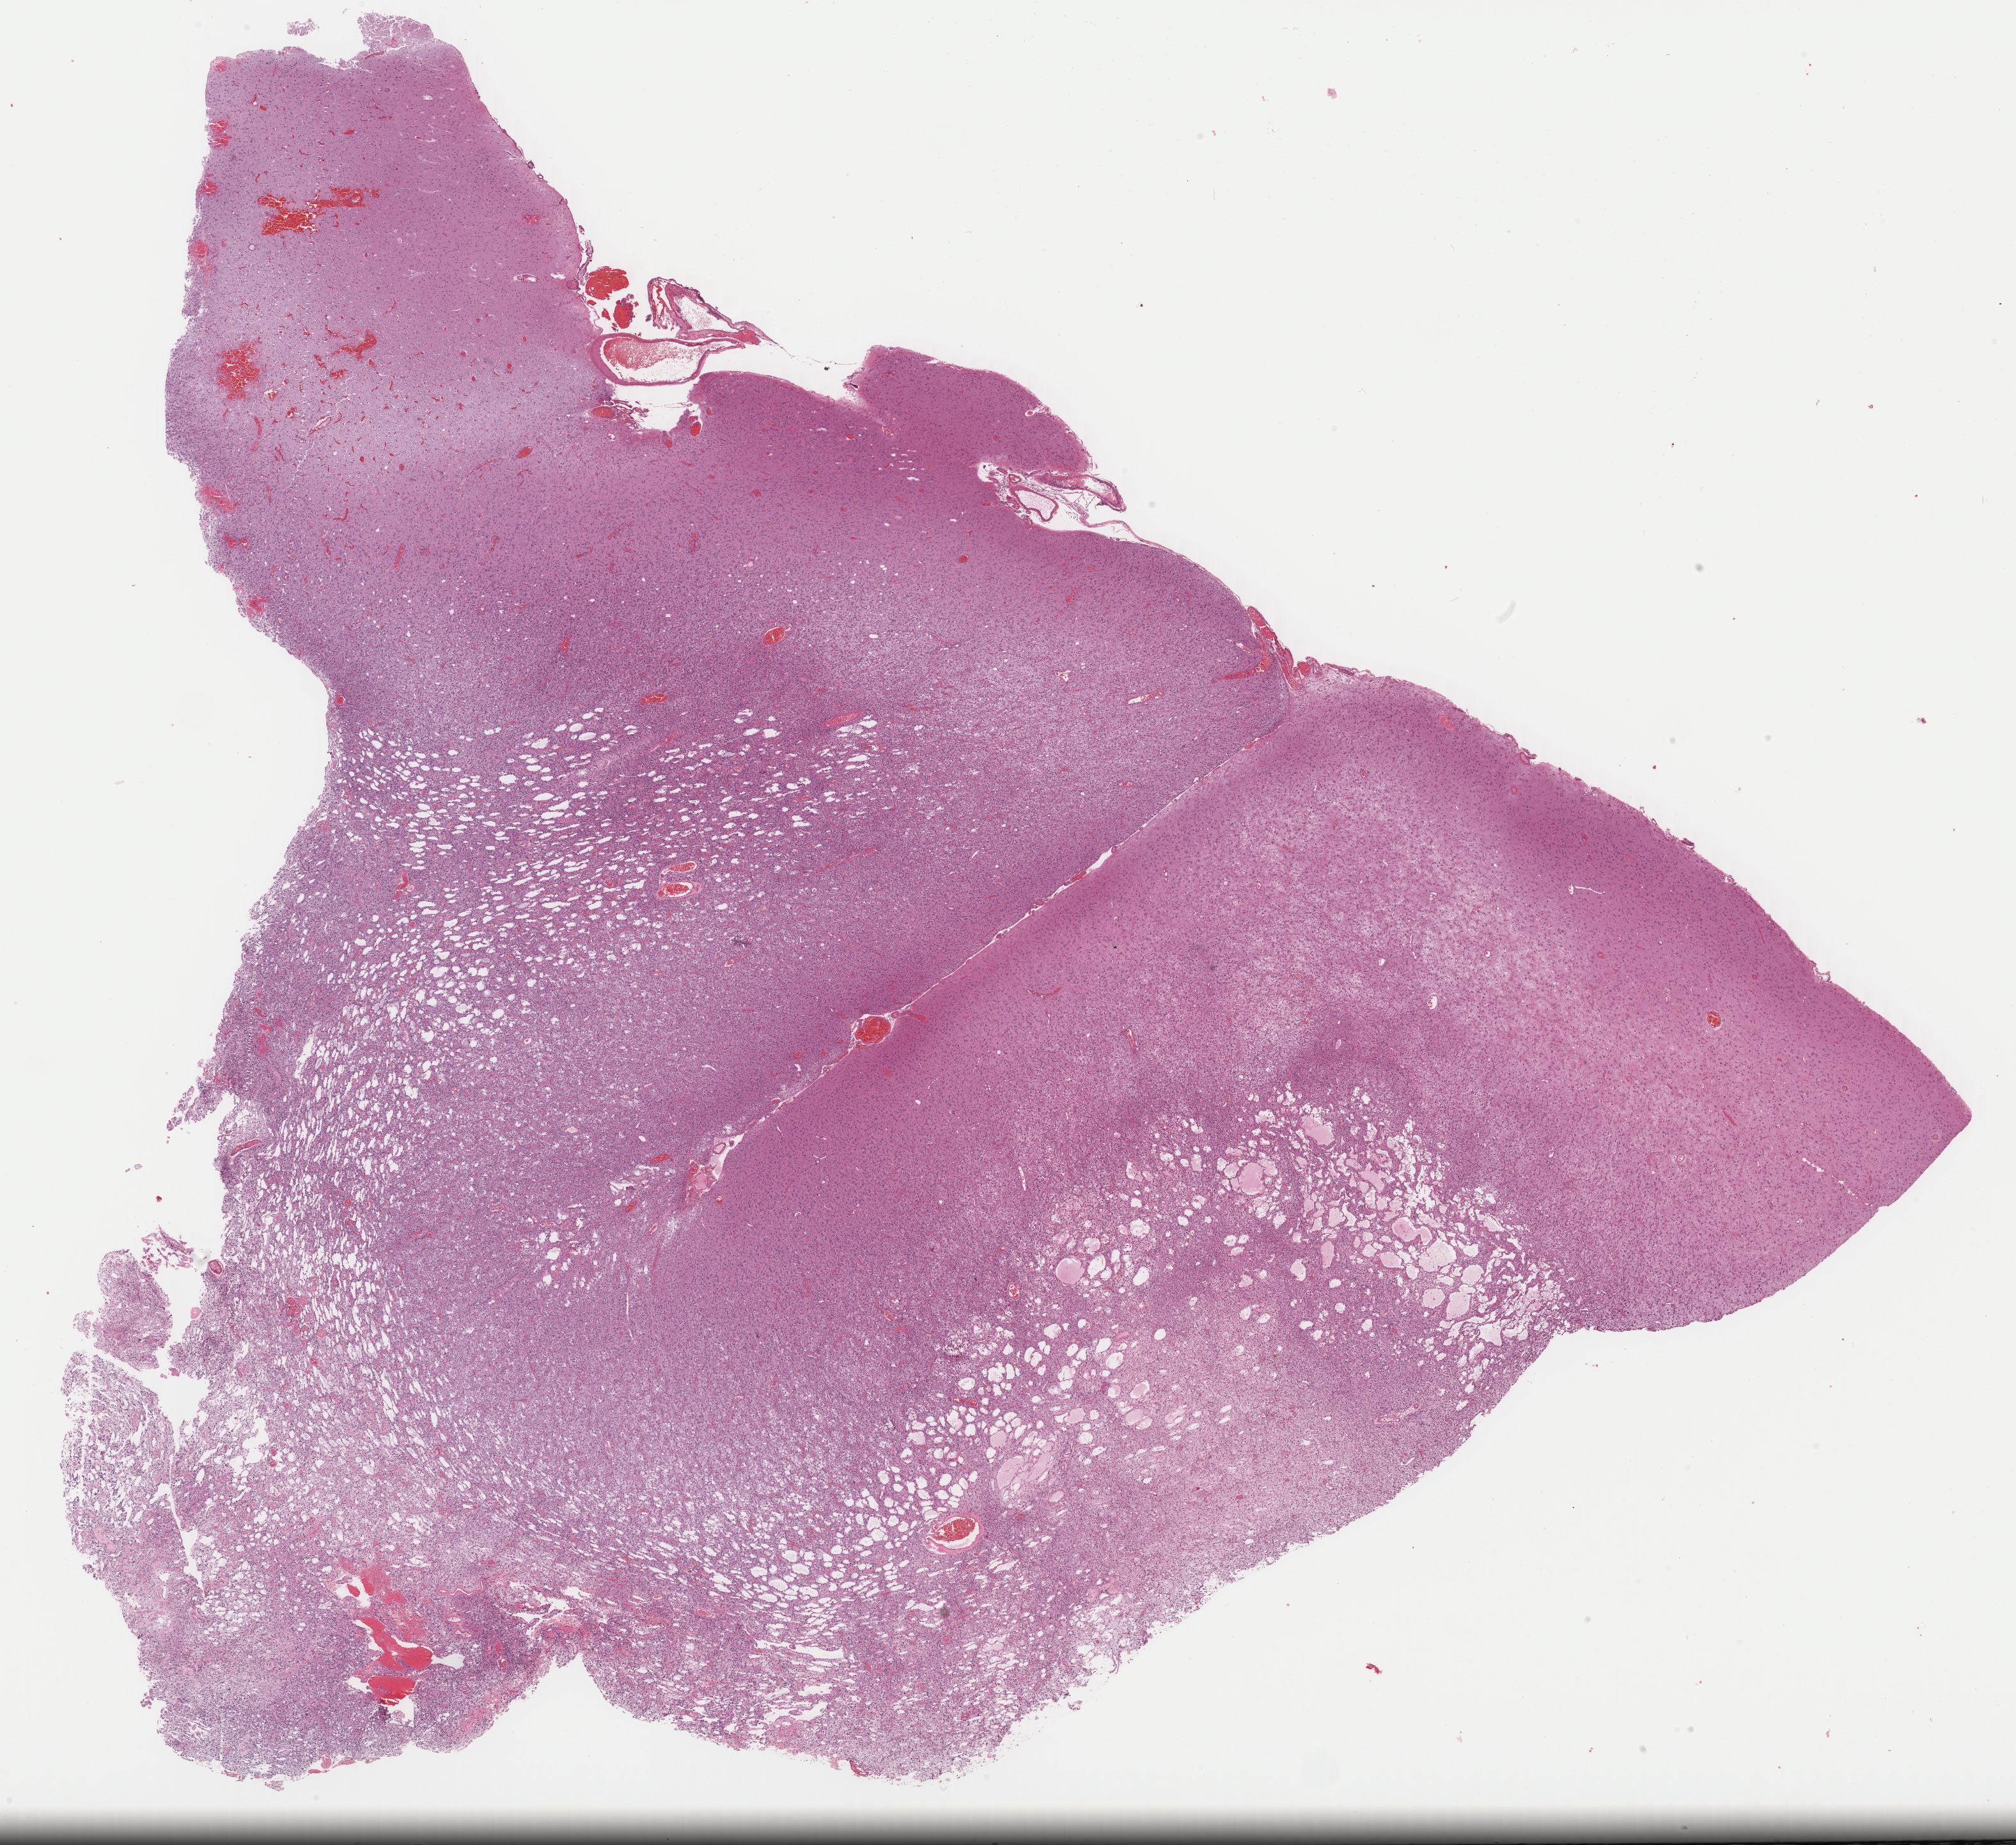
Whole-slide histology image, H&E, low-resolution overview of the scanned area, about 24.8 x 22.7 mm, formalin-fixed paraffin-embedded (FFPE) diagnostic section, primary tumour sample from the brain. Patient: male, age at initial diagnosis 61 years. Histologic grade: G3 (poorly differentiated).
Laterality: left. Diagnosis: Mixed glioma (cerebrum).